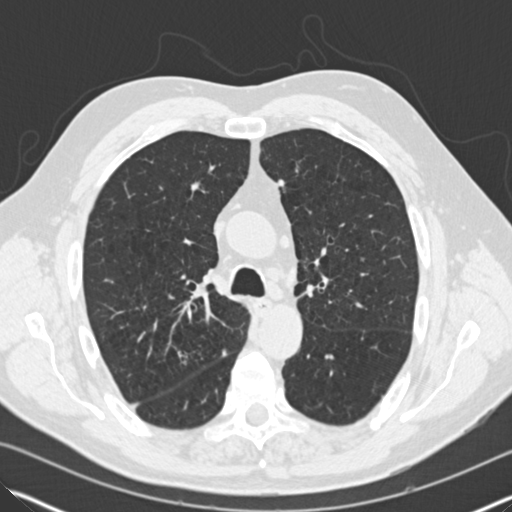
Low-dose screening chest CT, axial slice, baseline annual screen, lung window (W 1500 / L -600 HU), 2 mm slice thickness, slice 58 of 182 in the series. Male participant, aged 65 years at enrolment.
Lesion marked by an expert reader, bounding box <160,341,201,376> (left, top, right, bottom; pixels). The screening reader recorded 5 non-calcified nodules or masses ≥4 mm on this exam (left upper lobe, right upper lobe, right upper lobe, right lower lobe, right upper lobe); which of them this box marks is not recorded. Lung cancer was diagnosed 814 days after this screen (after the third annual screen): adenocarcinoma, NOS, right upper lobe, moderately differentiated (G2), stage IA (AJCC 6th edition), 16 mm at pathology.